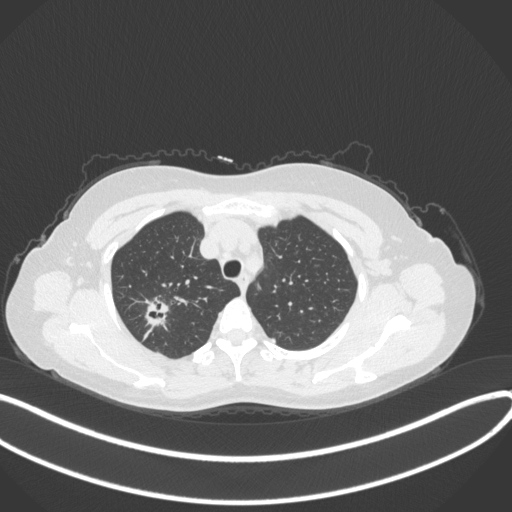
Chest CT, one axial slice; position 293 of 342 along the scan axis; 120 kVp; lung window (W 1500 / L -600 HU); 1 mm slice thickness; 512 × 512 image matrix, field of view 400 × 400 mm. Patient: female, 50 years. From the clinical record (not read from this slice): clinical TNM (as recorded): T1c N0 M0; histopathological grade: G2-3.
Structures marked on this image (rectangle marked by the reading radiologist):
- lung tumour (recorded histology: adenocarcinoma): bounding box <140,295,166,328> (left, top, right, bottom; pixels)